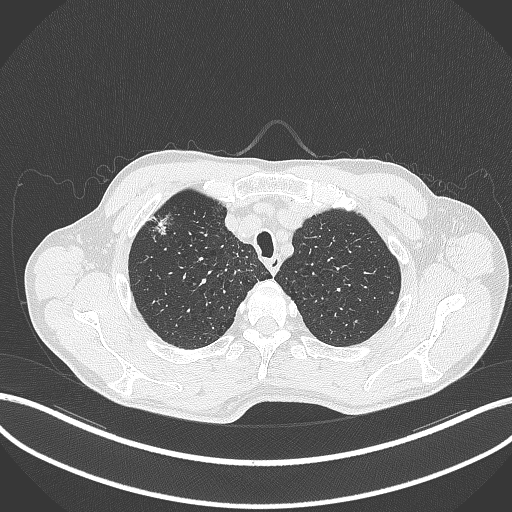
Chest CT, one axial slice; slice 358 of 427 in the series (ordered by position); 120 kVp; lung window (W 1500 / L -600 HU); 1 mm slice thickness; 512 × 512 image matrix. Patient: male, 69 years. From the clinical record (not read from this slice): clinical TNM (as recorded): T1b N1 M0.
Structures marked on this image (bounding box drawn by a radiologist):
- lung tumour (recorded histology: adenocarcinoma): bounding box (x1, y1, x2, y2) in pixels: (145, 210, 173, 238)